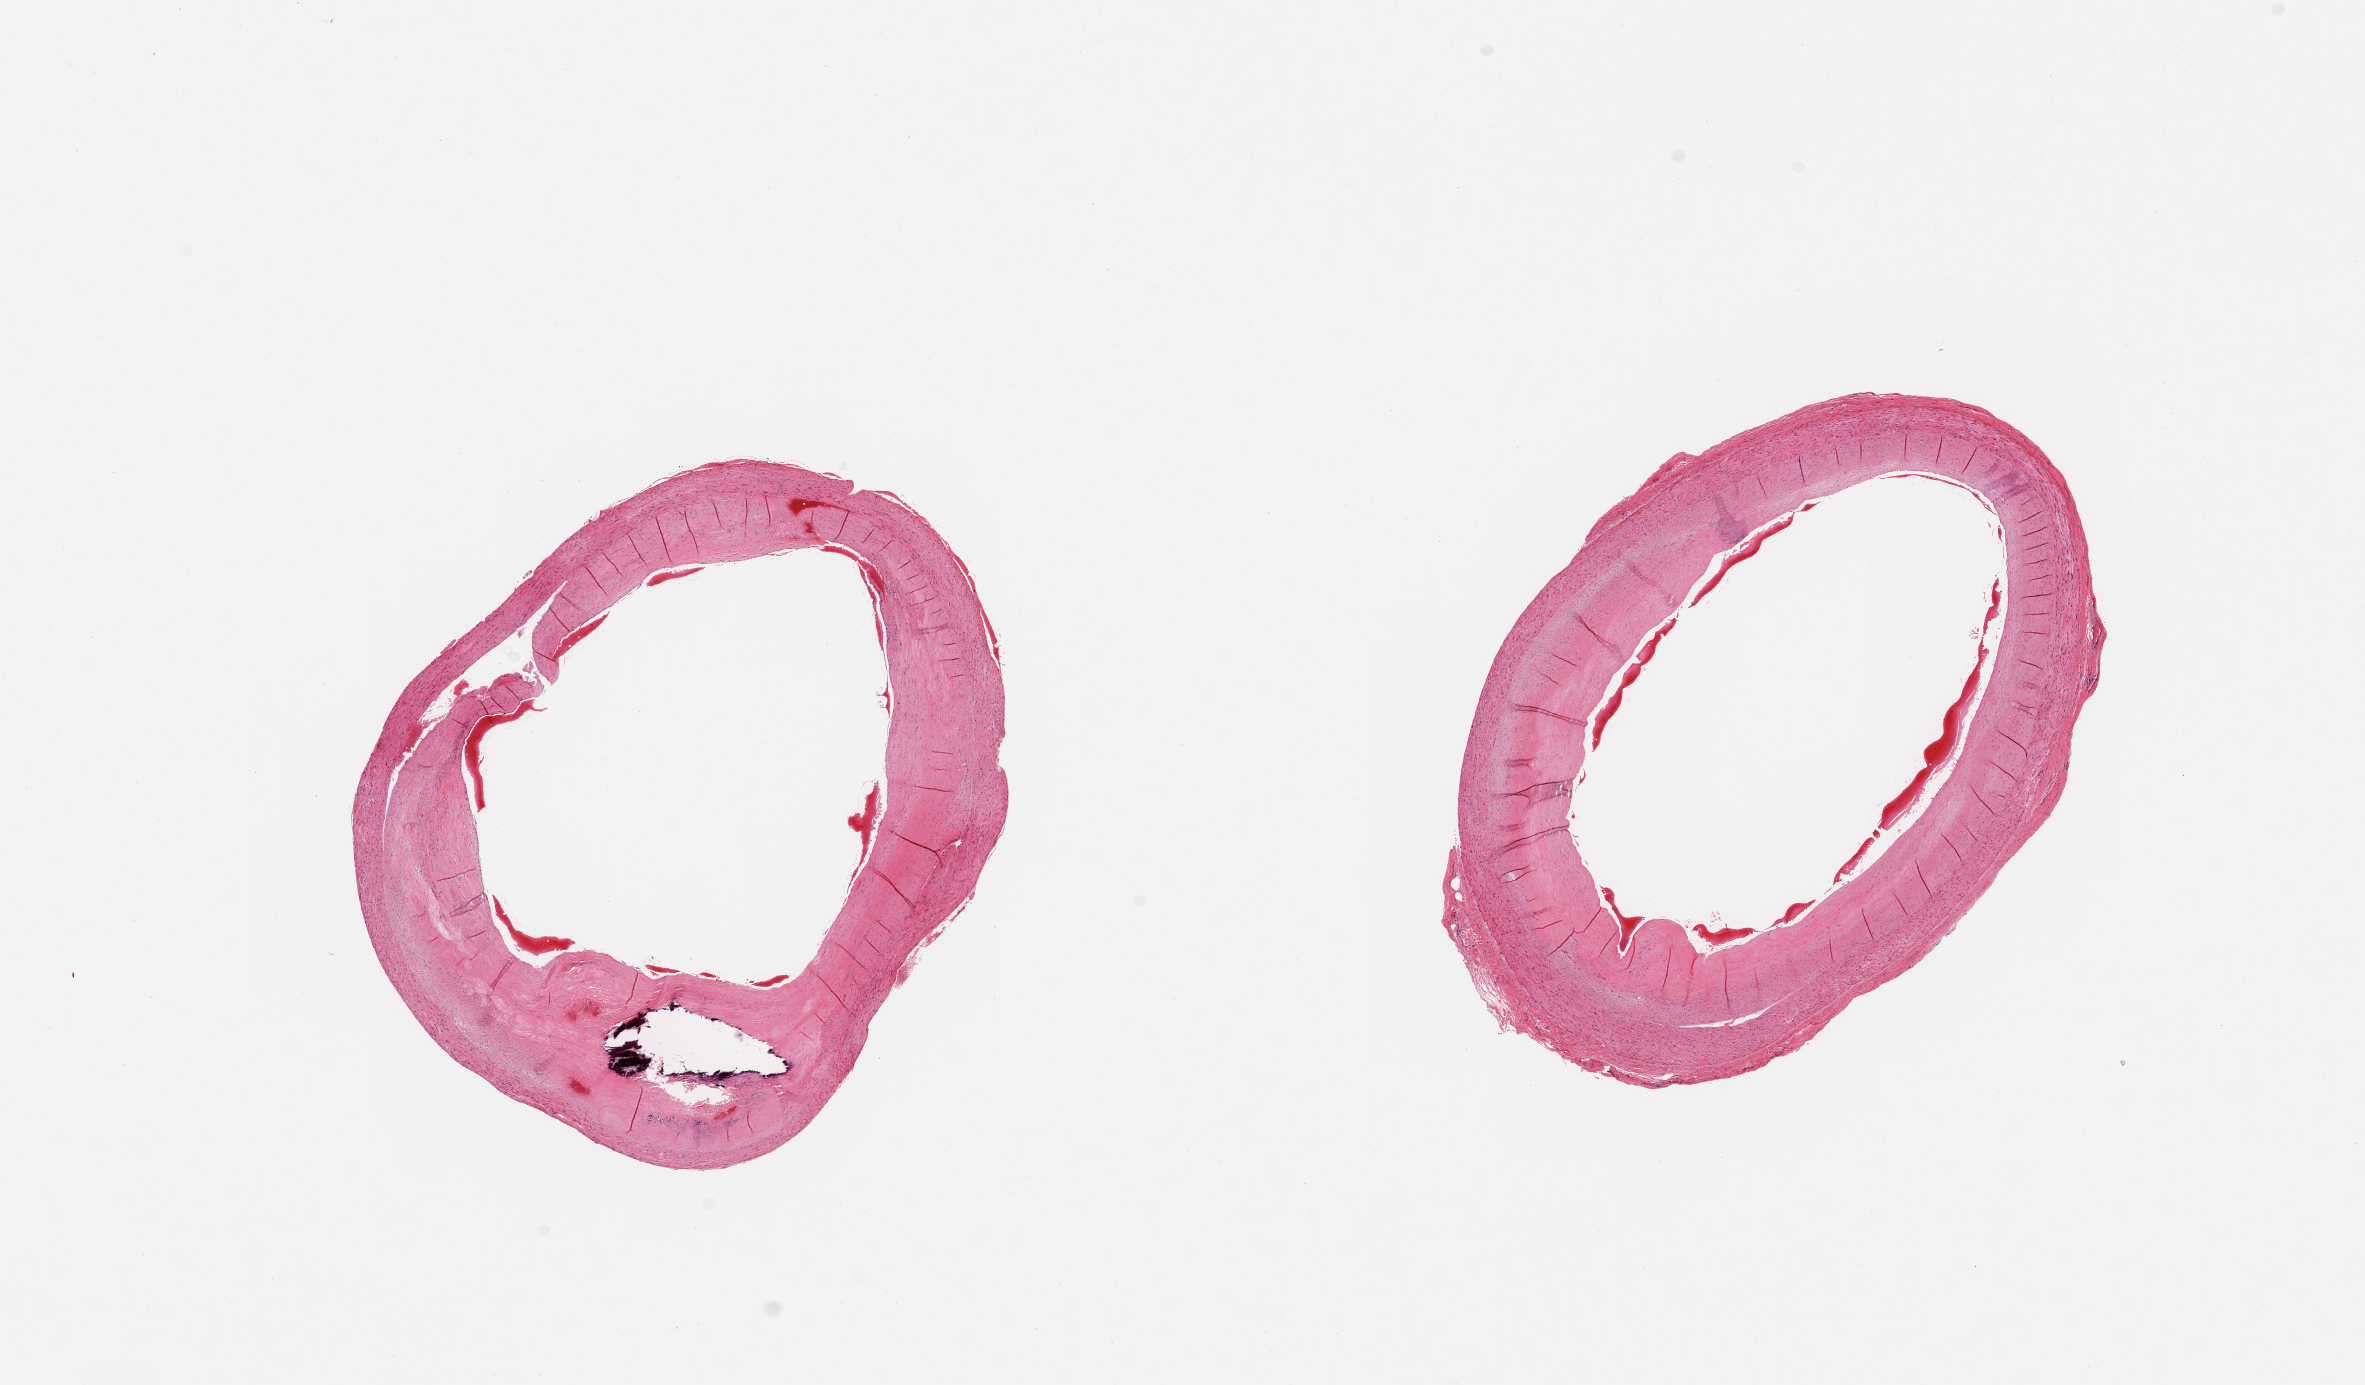
Haematoxylin and eosin whole-slide image — whole scanned area (about 18.7 x 11.0 mm, slide scanned at 20x) shown as a low-resolution overview; PAXgene-fixed paraffin-embedded (PFPE) section; sampled site (target tissue): coronary artery; donor tissue sample. Donor: male.
Review note (as recorded): 2 pieces; fibrosclerotic plaque with focal calcification; up to 0.3mm rim of adventitia.